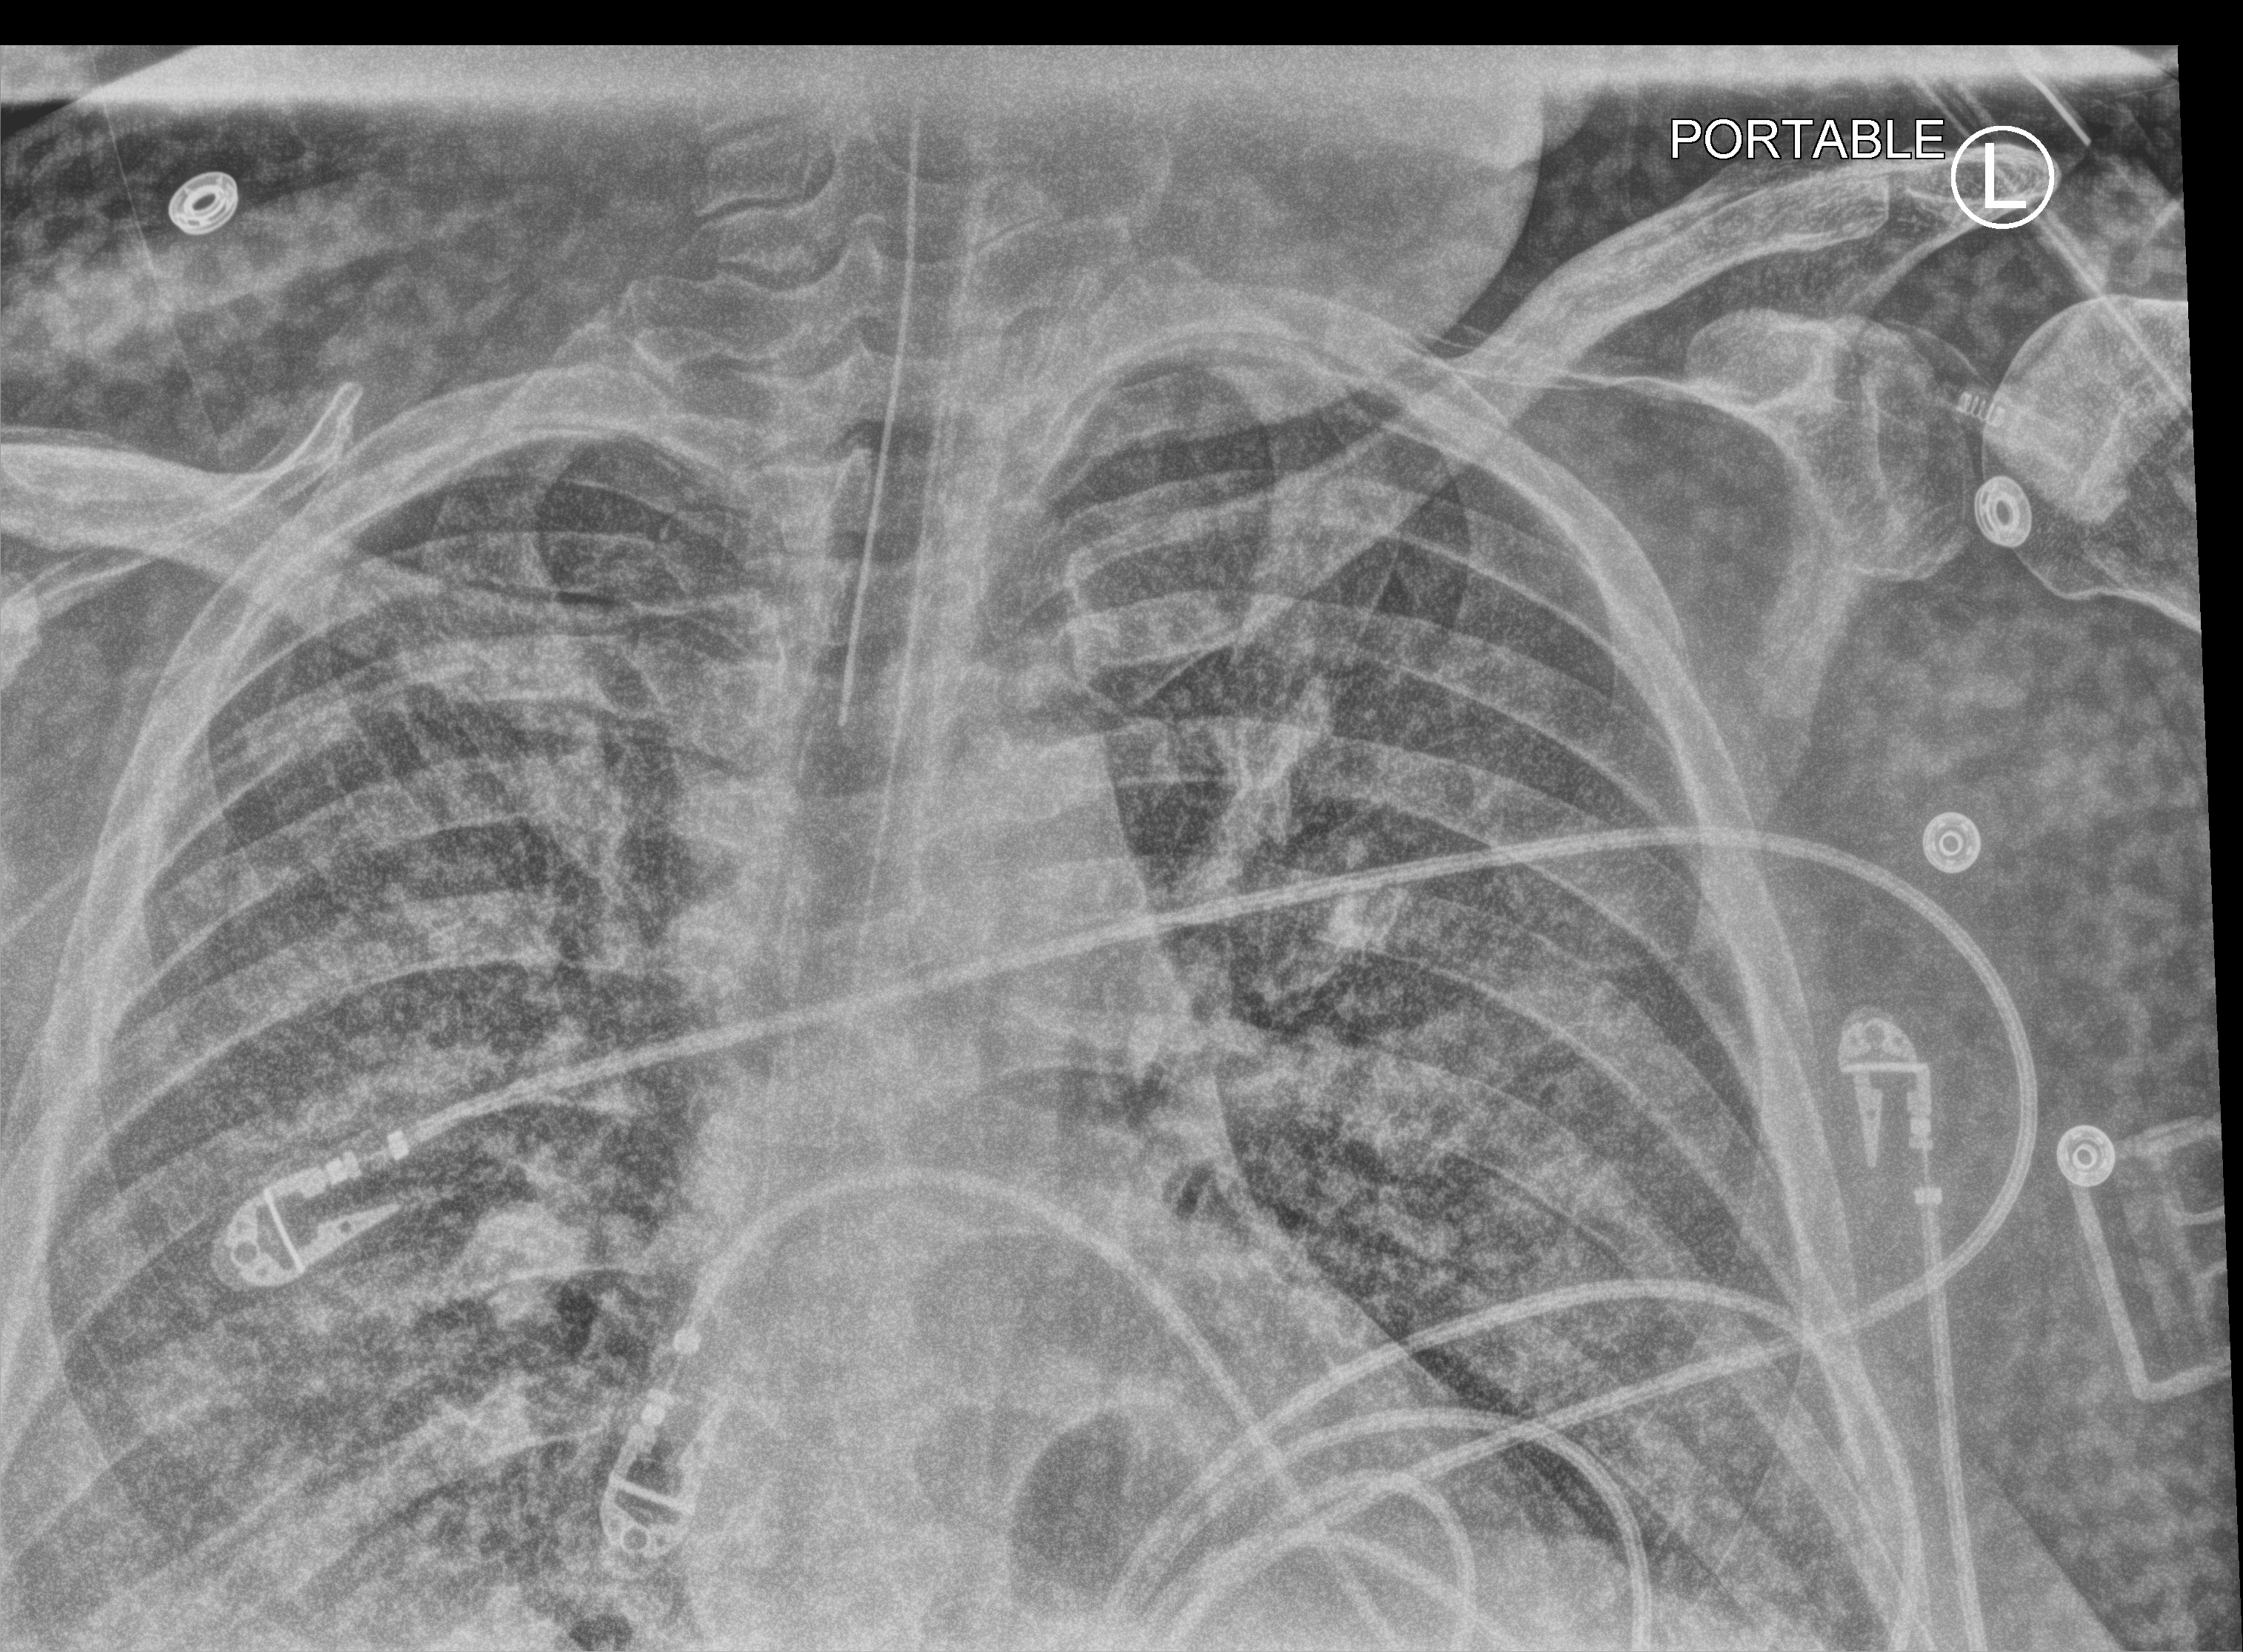
Chest X-ray (portable); anteroposterior (AP) projection. Adult patient hospitalised with COVID-19, age 18–59 years.
Admission-level facts for this patient (not findings on this image; timing relative to this image not recorded):
- admitted to intensive care during this hospital stay: yes
- mechanically ventilated during this hospital stay: yes